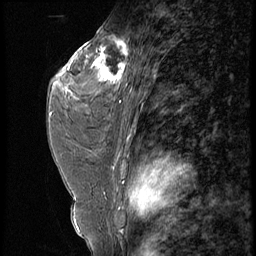
Breast MRI (dynamic contrast-enhanced), one sagittal slice. Position 34 of 56 along the scan axis. 4 images stored at this slice position (order not interpretable as contrast timing). 1.5 T. TE 4.2 ms, TR 9 ms. 2.5 mm slice thickness. 256 × 256 image matrix. Patient: female, 44 years. From the clinical record (not read from this slice): setting: breast cancer imaged before/during neoadjuvant chemotherapy; receptor status: triple-negative.
Annotated regions visible in this slice (semi-automatically segmented with operator editing):
- analysis volume of interest (the breast-tissue region the enhancement analysis was run in; not a lesion): bounding box (x1, y1, x2, y2) in pixels: (87, 28, 132, 99)
- tumour enhancement mask (voxels above the 140 % enhancement threshold inside the analysis volume of interest): (87, 38, 129, 88)